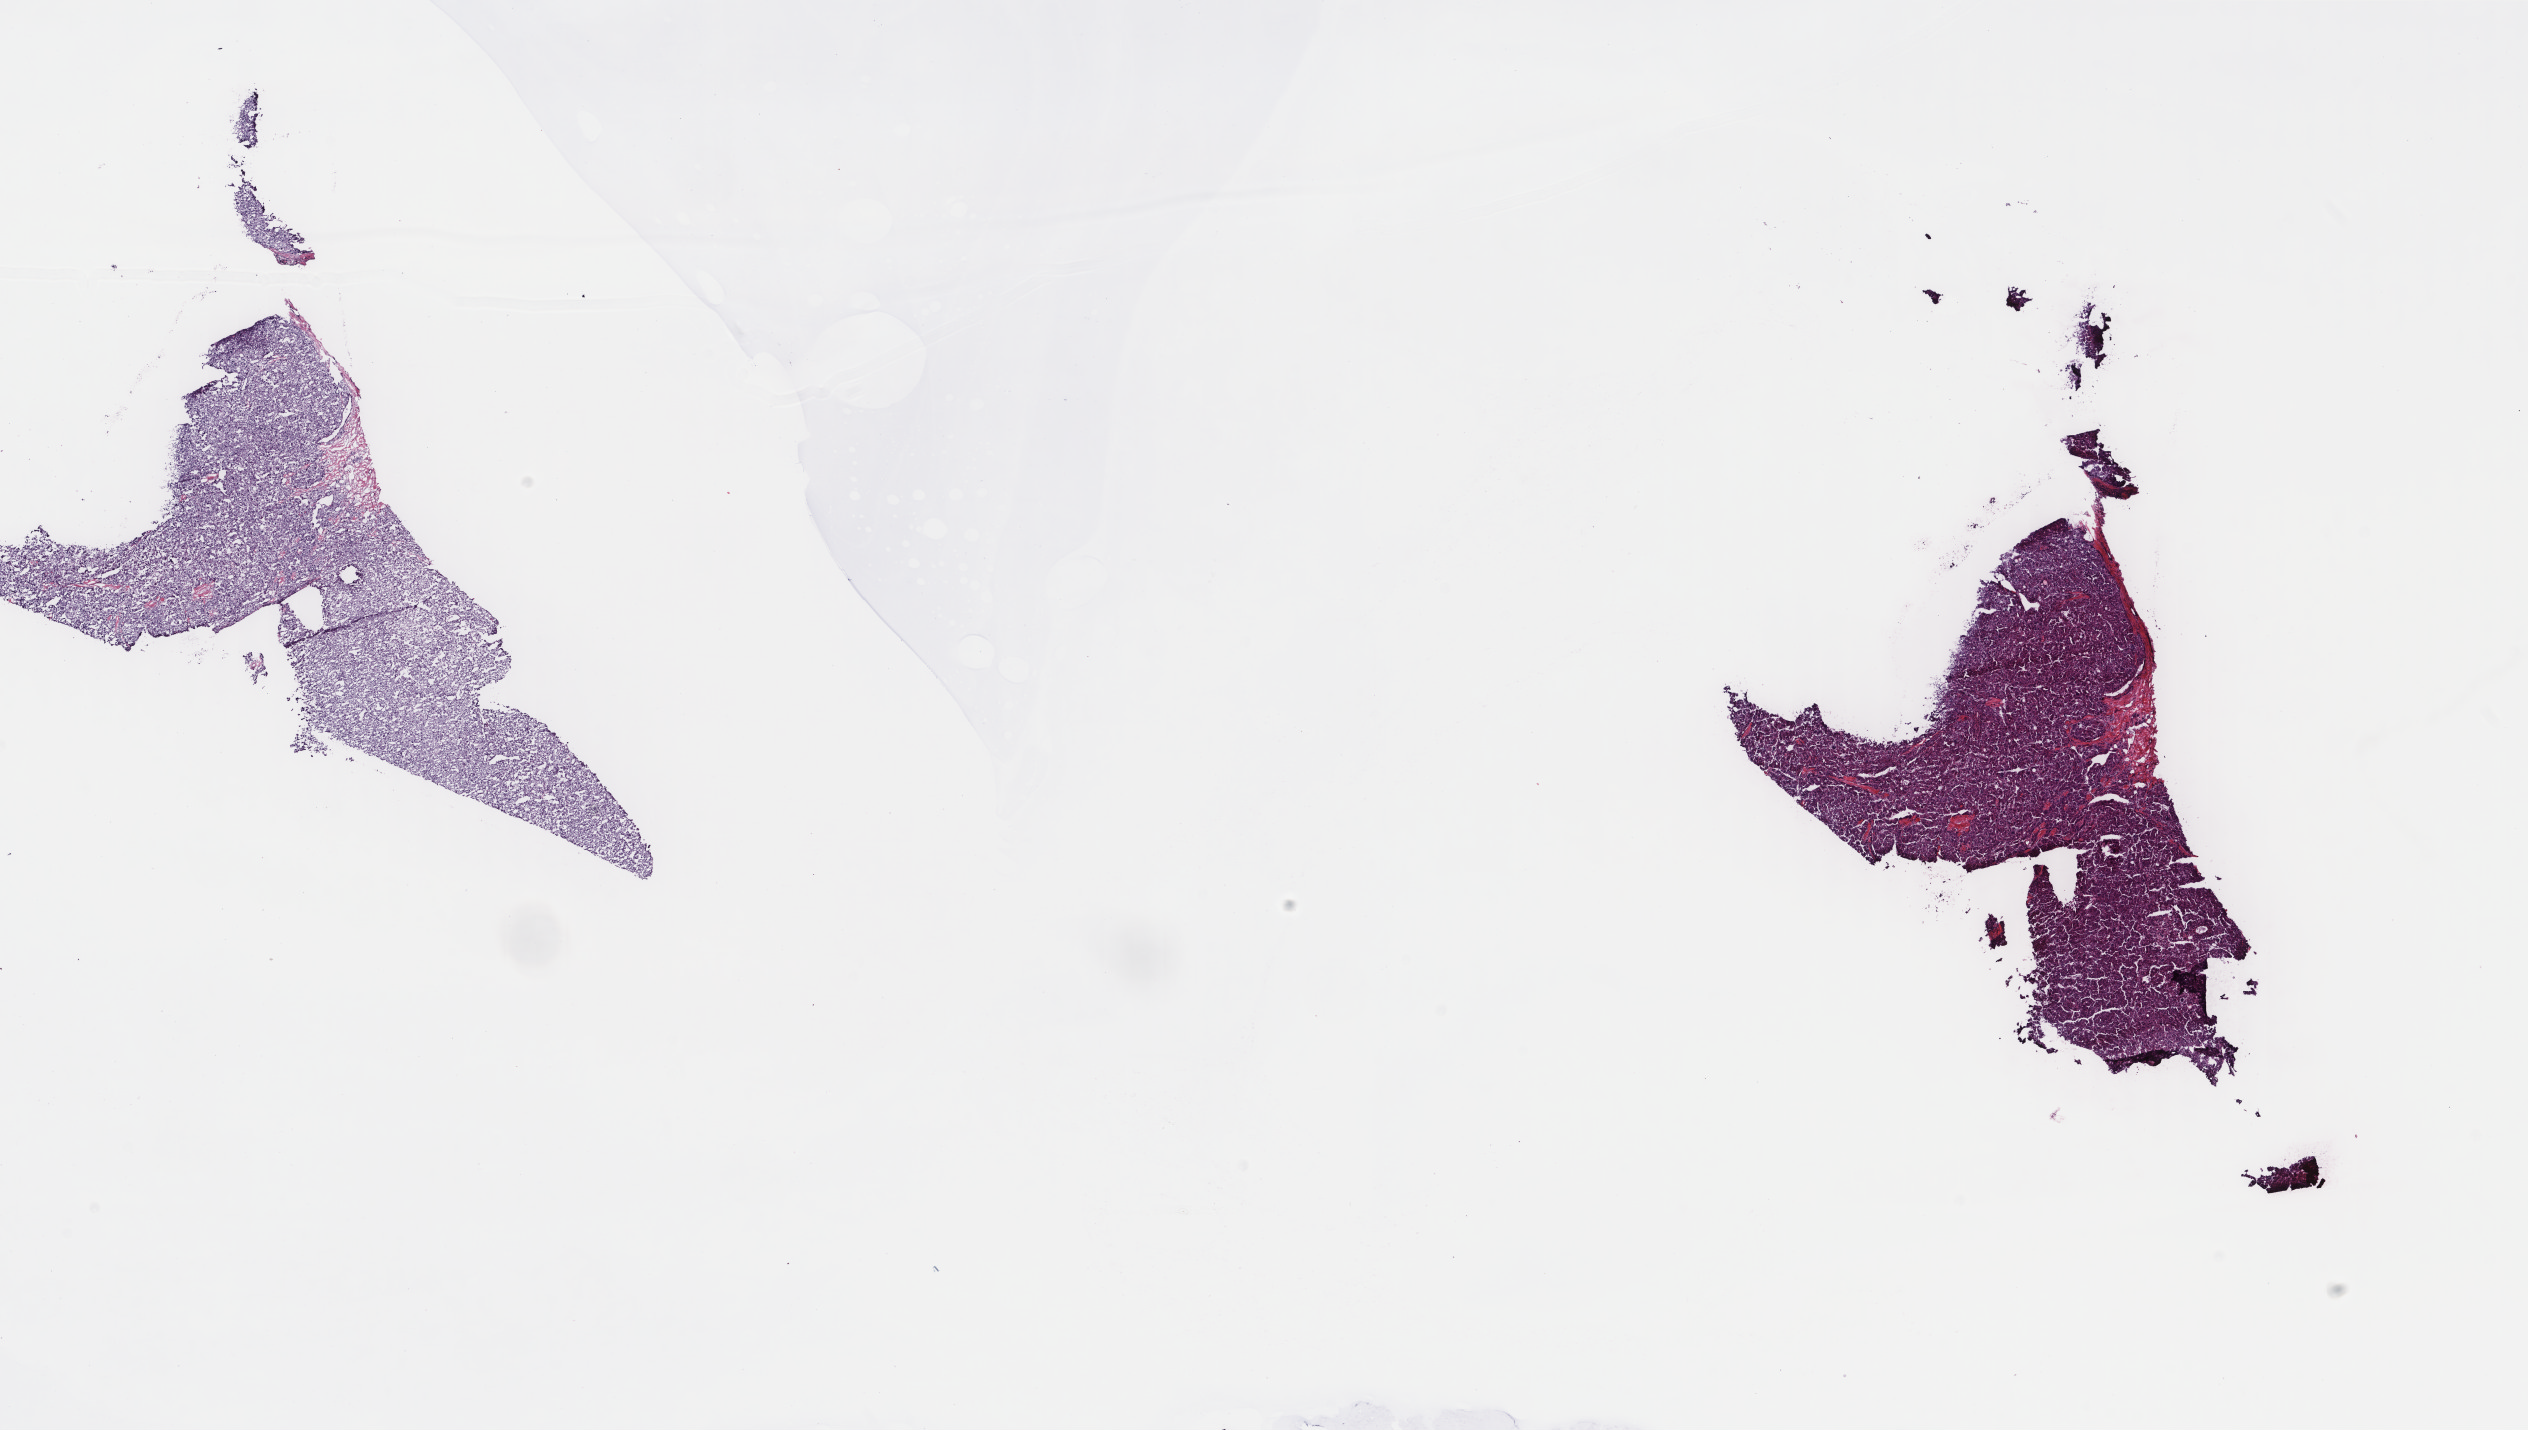
Digitized Hematoxylin and eosin (H&E) stained tissue section (whole slide) — shown as a low-resolution overview of the whole scanned area (about 20.1 x 11.4 mm, from a 40x scan), frozen section from the top of the tissue portion, sample: primary tumour, liver. Male patient; age at initial diagnosis 58 years. Histologic grade: G2 (moderately differentiated). Slide review estimates, as recorded: tumour cells 100%, tumour nuclei 95%, normal cells 0%, stromal cells 0%, necrosis 0%. Inflammatory infiltration, as recorded: lymphocyte infiltration 0%, monocyte infiltration 0%, neutrophil infiltration 0%.
* AJCC pathologic stage: I (7th edition)
* histologic diagnosis: Hepatocellular carcinoma, NOS